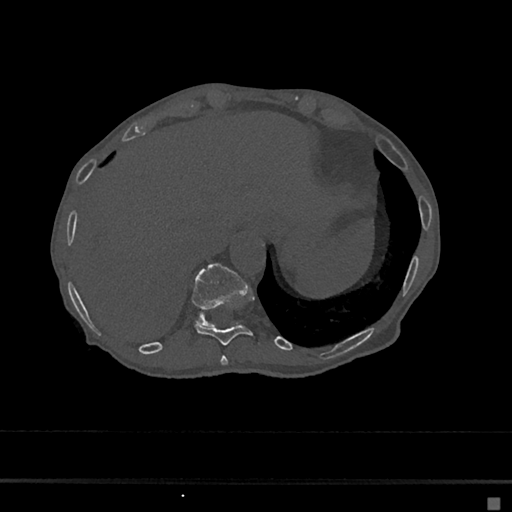
CT including the spine, one axial slice. Slice 210 of 797 in the series (ordered by position). 120 kVp. Bone window (W 1800 / L 400 HU). 512 × 512 image matrix. Patient: female, 68 years. From the clinical record (not read from this slice): primary cancer: renal.
Annotated regions visible in this slice (semi-automatic segmentation, software-assisted and operator-edited):
- T10 vertebra: bounding box (x1, y1, x2, y2) in pixels: (195, 324, 262, 346)
- T11 vertebra: (192, 263, 248, 326)
- T9 vertebra: (220, 355, 228, 366)